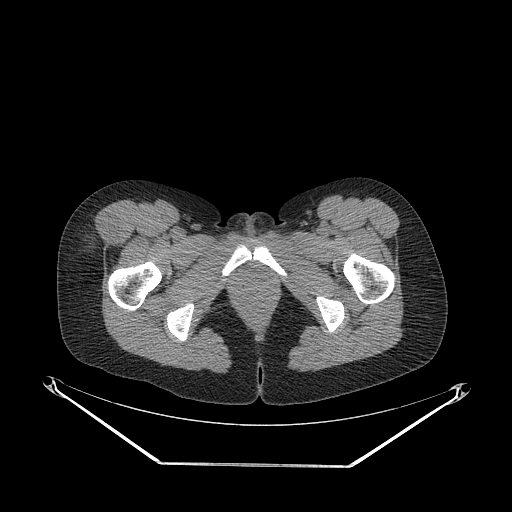
CT of an extremity soft-tissue mass (from a PET/CT study), one axial slice. Slice 55 of 267 in the series (ordered by position). Reconstruction kernel STANDARD. 140 kVp. Soft-tissue window (W 400 / L 40 HU). 3.75 mm slice thickness. 512 × 512 image matrix, field of view 500 × 500 mm. Female patient. From the clinical record (not read from this slice): histological type: synovial sarcoma; grade: intermediate; site of the primary tumour: right thigh.
Structures marked on this image (expert contour drawn on MRI and transferred to this co-registered scan by the dataset authors):
- gross tumour volume including surrounding oedema: bounding box (x1, y1, x2, y2) in pixels: (82, 215, 118, 250)
- gross tumour volume (mass): (82, 215, 118, 252)